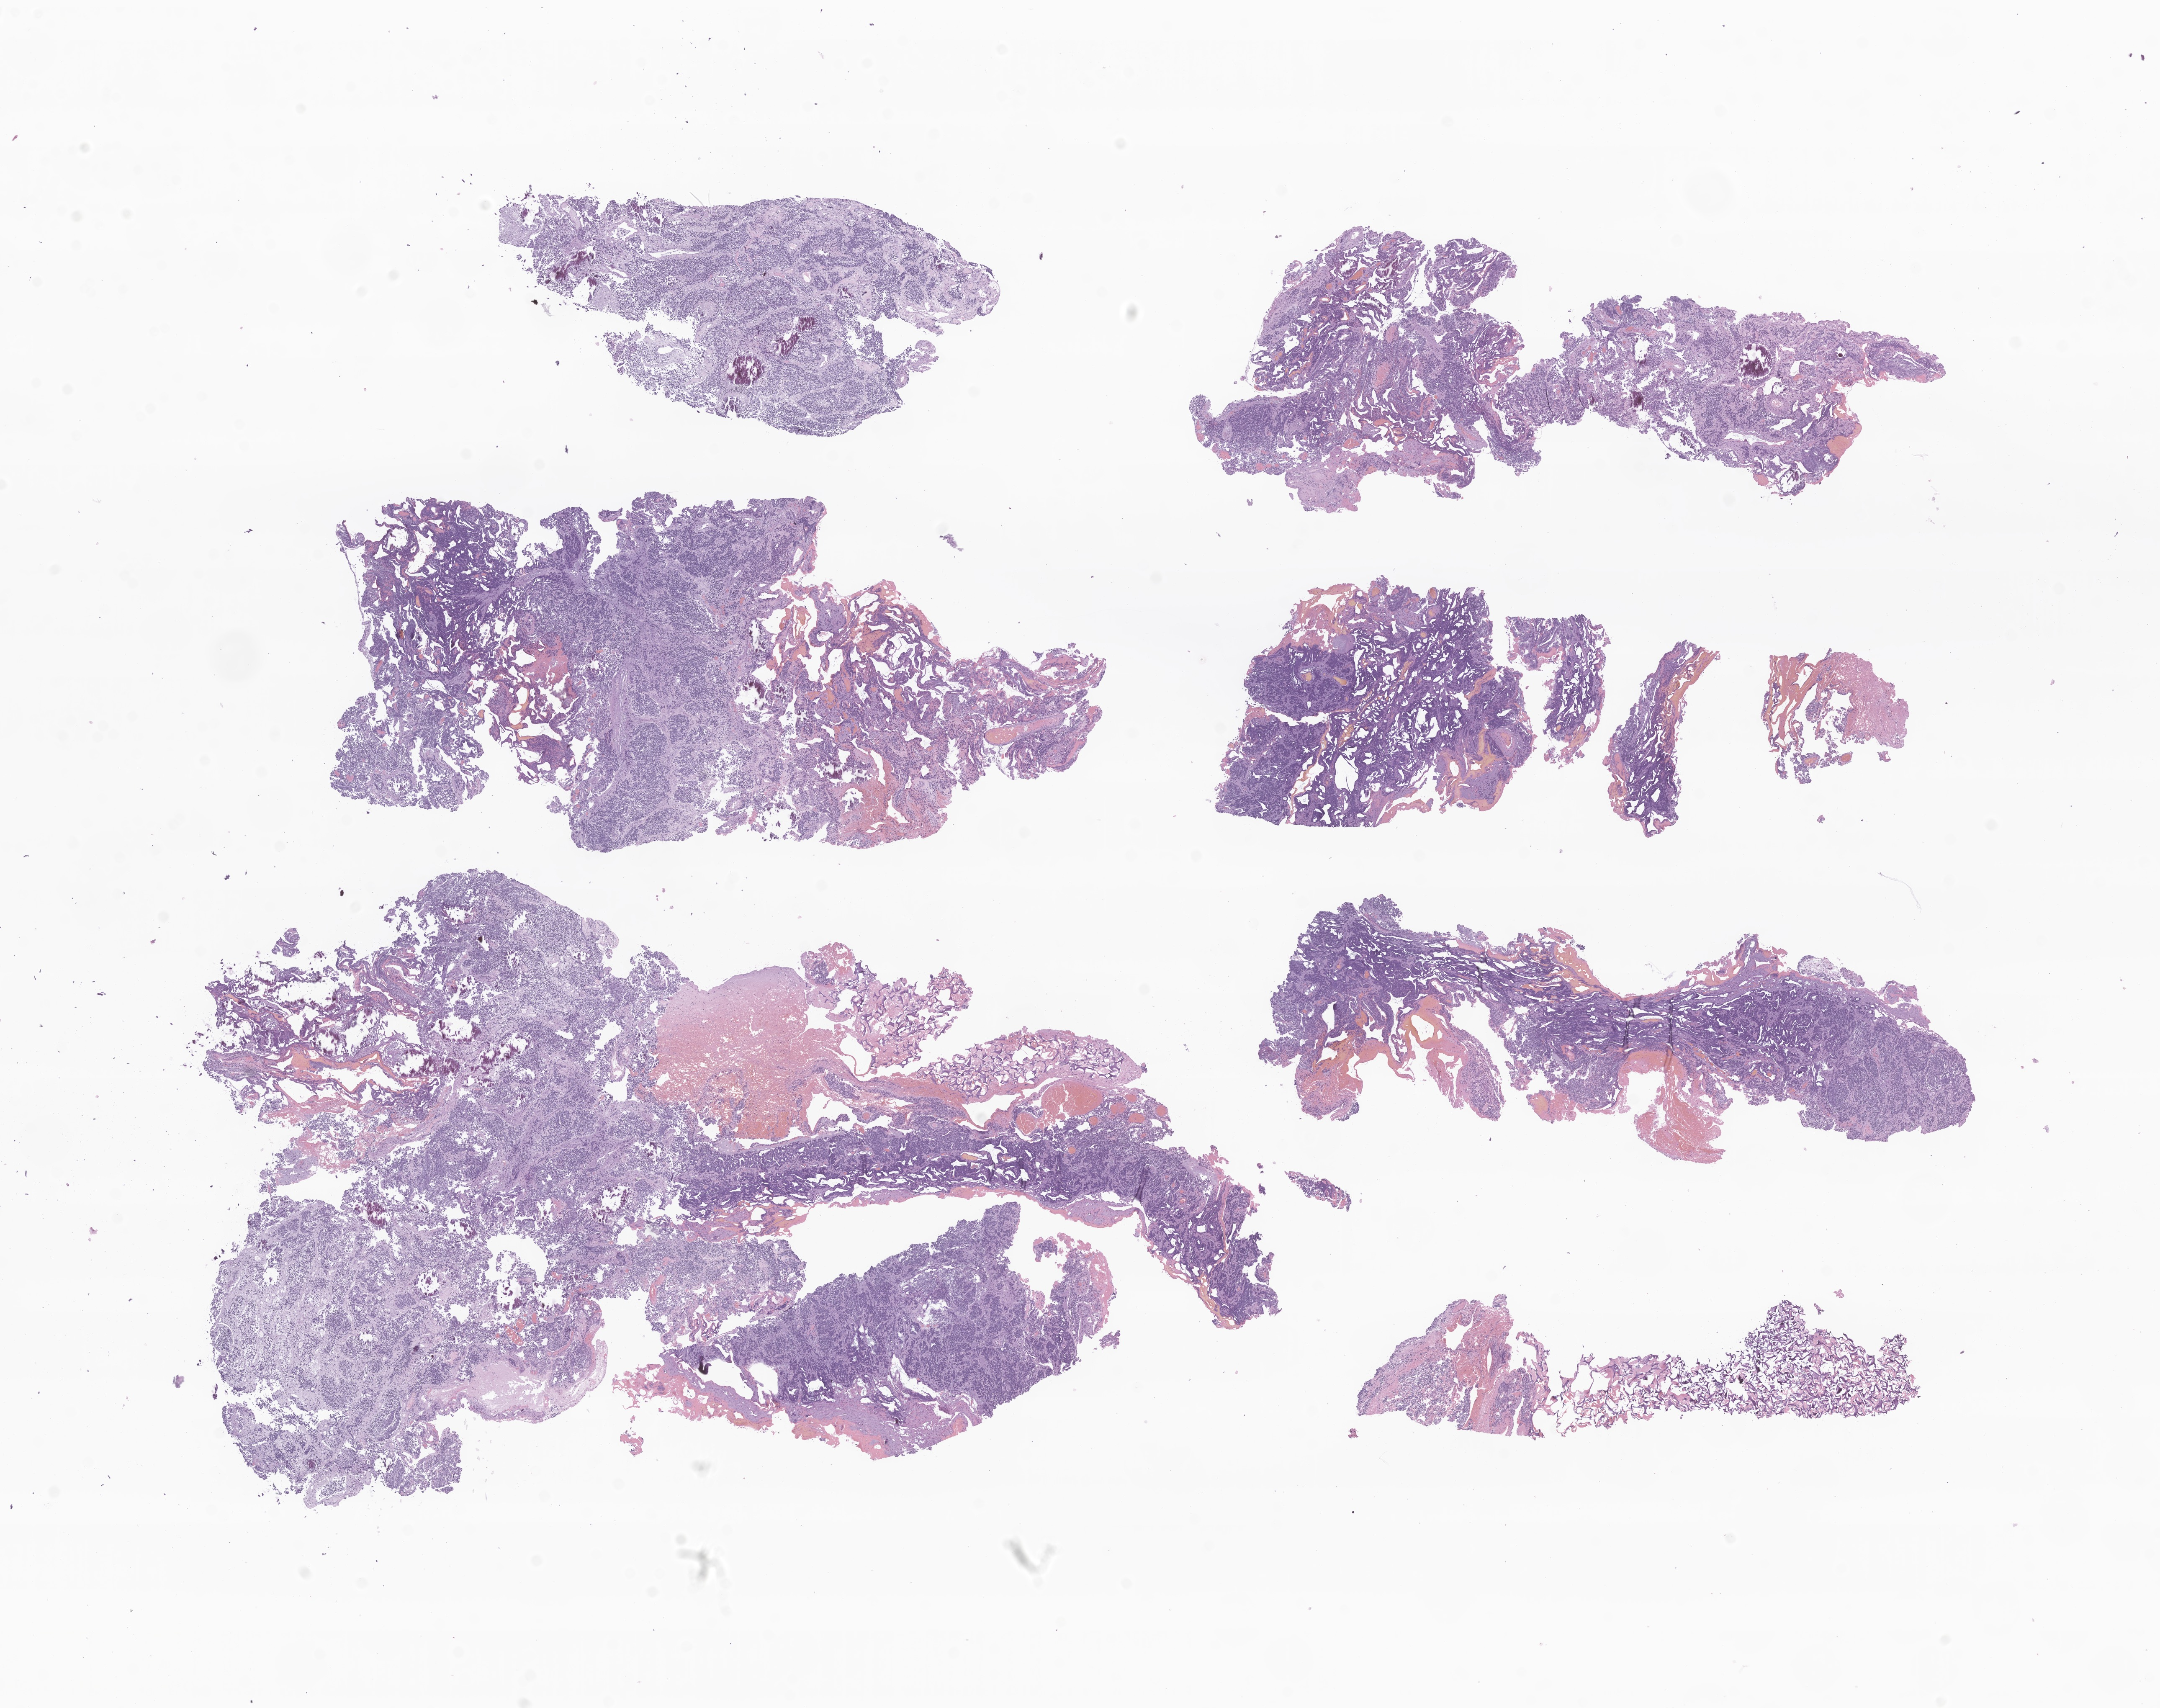
Whole-slide image, haematoxylin and eosin stain of tumor tissue from the pineal gland, shown as a low-resolution overview of the whole scanned area (about 21.8 x 17.2 mm), formalin-fixed paraffin-embedded section. Patient: male, age 152 months (12 years 8 months).
Diagnosis (ICD-O-3 morphology term): Pineoblastoma.